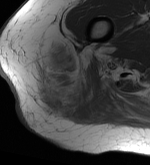
MRI of an extremity soft-tissue mass, one axial slice; slice 14 of 56 in the series (ordered by position); MR volume resampled by the dataset authors to the PET/CT grid (not the native acquisition matrix); 150 × 165 image matrix, field of view 146 × 161 mm. Female patient. Case-level facts recorded for this patient, not image findings: histological type: epithelioid sarcoma with vascular differentiation; site of the primary tumour: right buttock.
Outlined on this slice (expert contour drawn on MRI and transferred to this co-registered scan by the dataset authors):
- gross tumour volume (mass): bounding box [x1, y1, x2, y2] px = [36, 44, 90, 119]